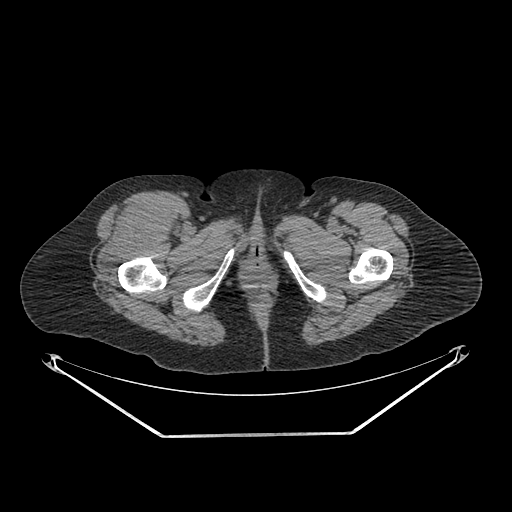
CT of an extremity soft-tissue mass (from a PET/CT study), one axial slice. Reconstruction kernel SOFT. 140 kVp. Soft-tissue window (W 400 / L 40 HU). 512 × 512 image matrix, field of view 500 × 500 mm. Female patient. From the clinical record (not read from this slice): histological type: pleiomorphic undifferentiated sarcoma; grade: high; site of the primary tumour: right quadricep.
Outlined on this slice (expert contour drawn on MRI and transferred to this co-registered scan by the dataset authors):
- tumour plus oedema (research contour): bounding box (x1, y1, x2, y2) in pixels: (101, 201, 170, 270)
- tumour (research contour): (101, 201, 170, 270)